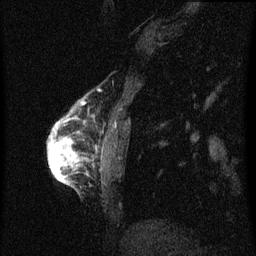
Breast MRI (dynamic contrast-enhanced), one sagittal slice. Dynamic contrast-enhanced series, image 2 of 3 at this slice position (ordered by acquisition). 1.5 T. TE 4.2 ms, TR 8 ms. 2 mm slice thickness. 256 × 256 image matrix, field of view 180 × 180 mm. Patient: female, 56 years.
Annotated regions visible in this slice (semi-automatically segmented with operator editing):
- analysis volume of interest (the breast-tissue region the enhancement analysis was run in; not a lesion): bounding box <48,112,81,185> (left, top, right, bottom; pixels)
- tumour enhancement mask (voxels above the 70 % enhancement threshold inside the analysis volume of interest): <48,122,79,183>